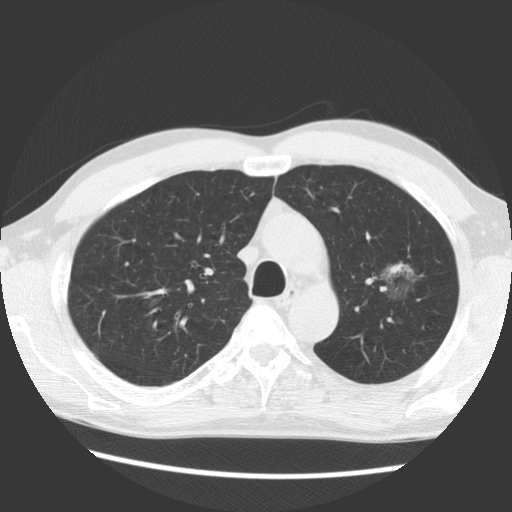
Low-dose screening chest CT, axial slice; baseline annual screen; lung window (W 1500 / L -600 HU); 2.5 mm slice thickness; standard (soft-tissue) reconstruction kernel (STANDARD); slice 98 of 138 in the series. Male, age 61 years at enrolment.
• Expert-annotated lung lesion, box from (x=356, y=239) to (x=441, y=314) px.
• Screening reader's record for this exam (one nodule recorded; not confirmed to be the boxed lesion): non-calcified nodule or mass ≥4 mm, left upper lobe, 17 × 14 mm, soft tissue attenuation.
• Lung cancer was diagnosed 1061 days after this screen (after the third annual screen): bronchiolo-alveolar adenocarcinoma, NOS, left upper lobe, well differentiated (G1), stage IB (AJCC 6th edition), 44 mm at pathology.